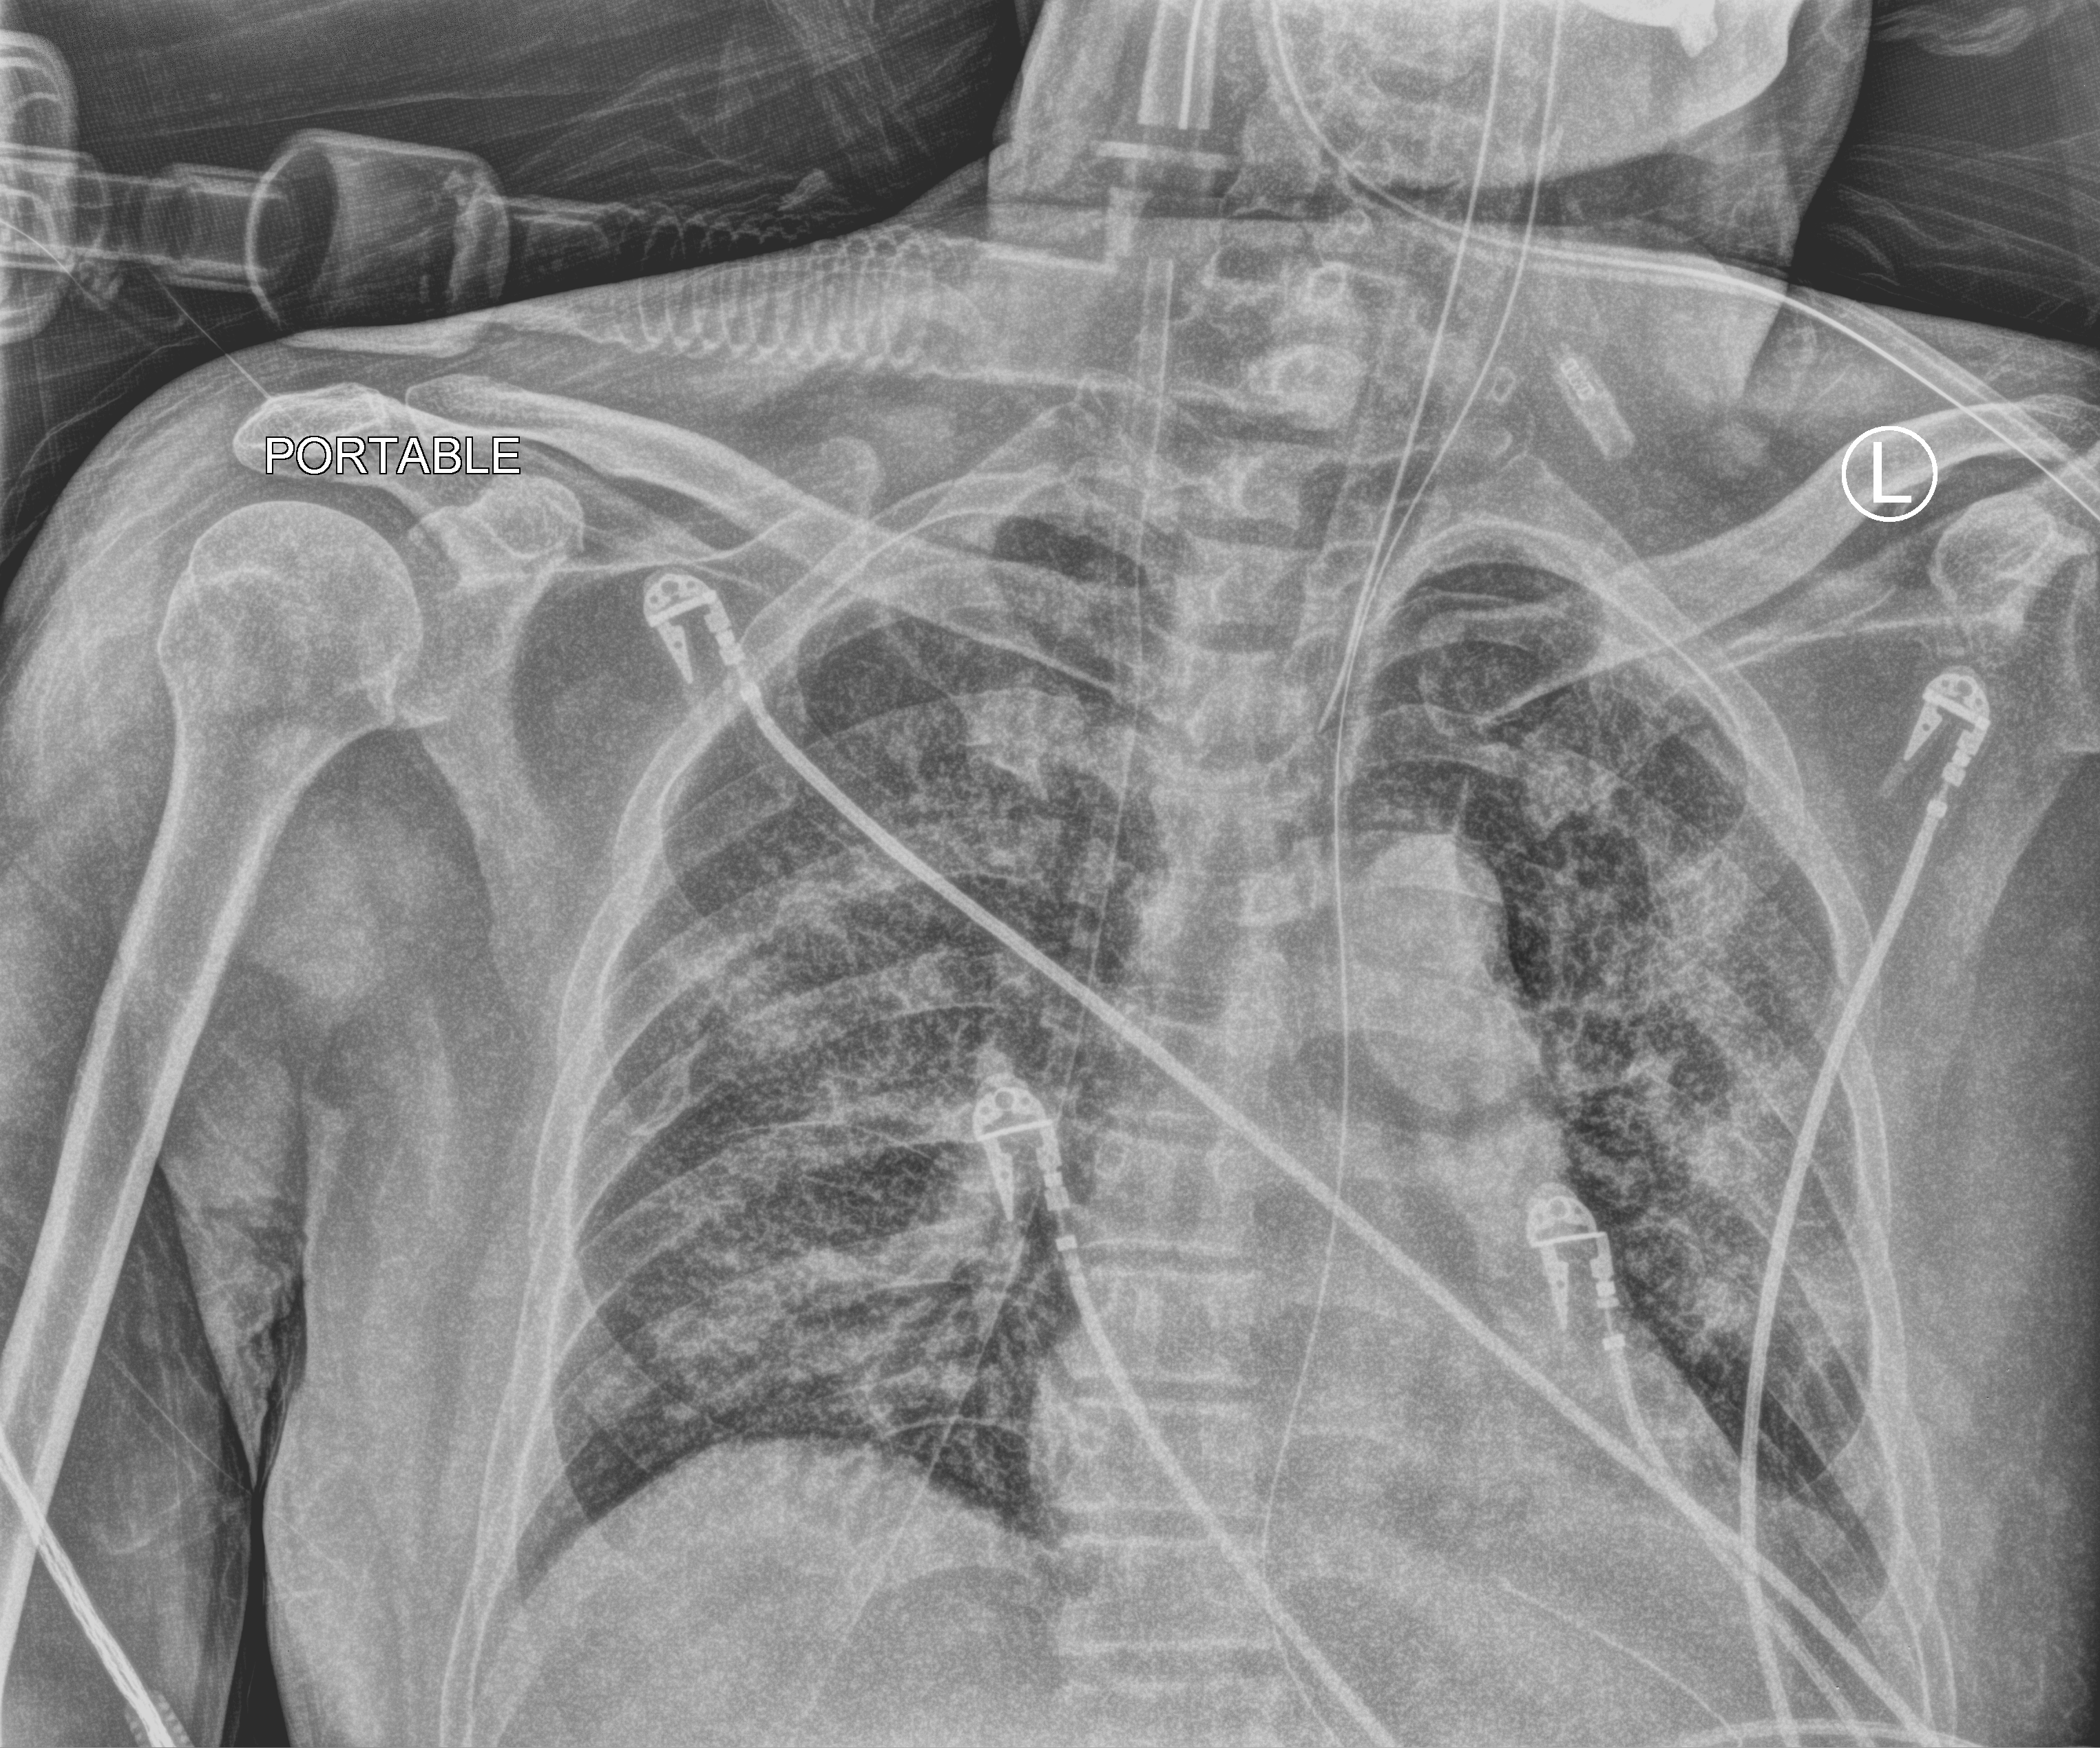
Chest X-ray (portable); anteroposterior (AP) projection. Male patient hospitalised with COVID-19, age 60–74 years.
Admission-level facts for this patient (not findings on this image; timing relative to this image not recorded): admitted to intensive care during this hospital stay: yes; mechanically ventilated during this hospital stay: yes.